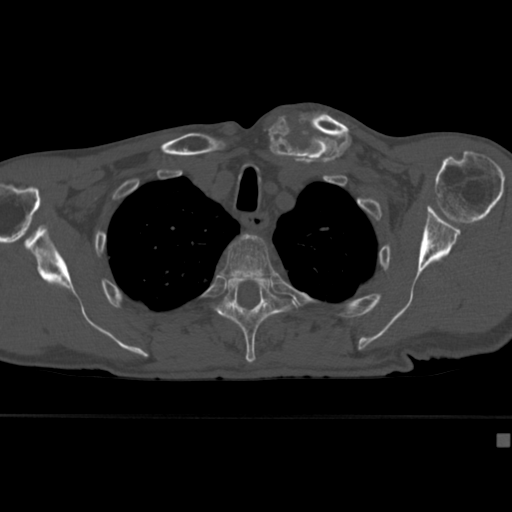
CT including the spine, one axial slice; slice 324 of 430 in the series (ordered by position); reconstruction kernel Br40s; bone window (W 1800 / L 400 HU); 1.5 mm slice thickness; 512 × 512 image matrix. Patient: male, 64 years. From the clinical record (not read from this slice): primary cancer: uterus.
Annotated regions visible in this slice (semi-automatically segmented with operator editing):
- T3 vertebra: bounding box [x1, y1, x2, y2] px = [222, 233, 277, 280]
- T4 vertebra: [214, 278, 298, 364]